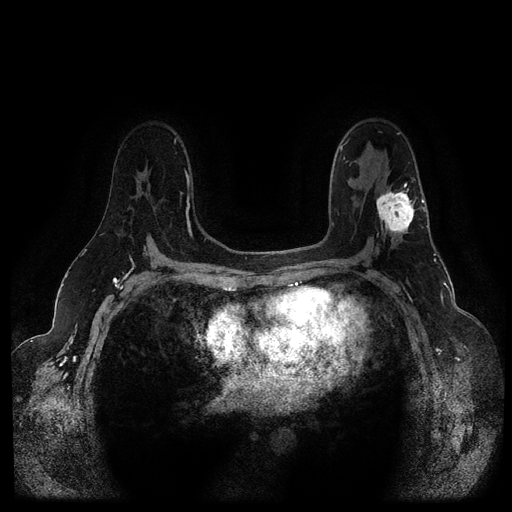
Breast MRI (dynamic contrast-enhanced, multi-phase), one axial slice; position 66 of 116 along the scan axis; dynamic contrast-enhanced series, time point 2 of 5 at this slice position (early post-contrast); 1.5 T; TE 2.6 ms, TR 5.3 ms; 2 mm slice thickness; 512 × 512 image matrix. Female patient, age 54 years.
Outlined on this slice (semi-automatic segmentation, software-assisted and operator-edited):
- breast lesion (labelled 'tumour' in the annotation; benign lesions carry a separate 'benign' label): bounding box (x1, y1, x2, y2) in pixels: (375, 185, 420, 236)